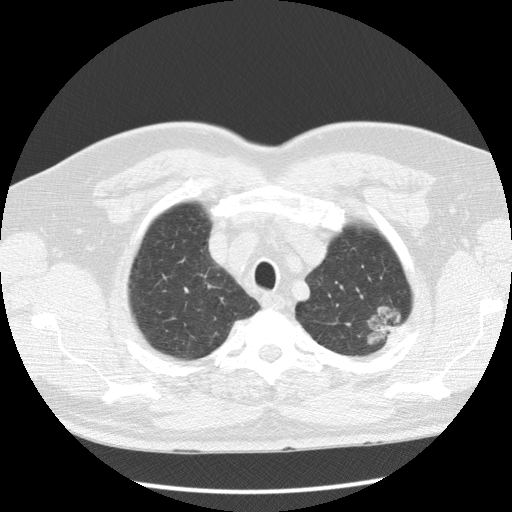
Low-dose screening chest CT, axial slice; baseline screening round; lung window (W 1500 / L -600 HU); 2.5 mm slice thickness; slice 17 of 123 in the series. Male participant, aged 60 years at enrolment.
Lesion marked by an expert reader, bounding box <349,294,413,354> (left, top, right, bottom; pixels). The screening reader recorded 3 non-calcified nodules or masses ≥4 mm on this exam (left upper lobe, right upper lobe, left upper lobe); which of them this box marks is not recorded. Official screen result: positive, change unspecified: nodule(s) >= 4 mm or enlarging nodule(s), mass(es), or other non-specific abnormalities suspicious for lung cancer.